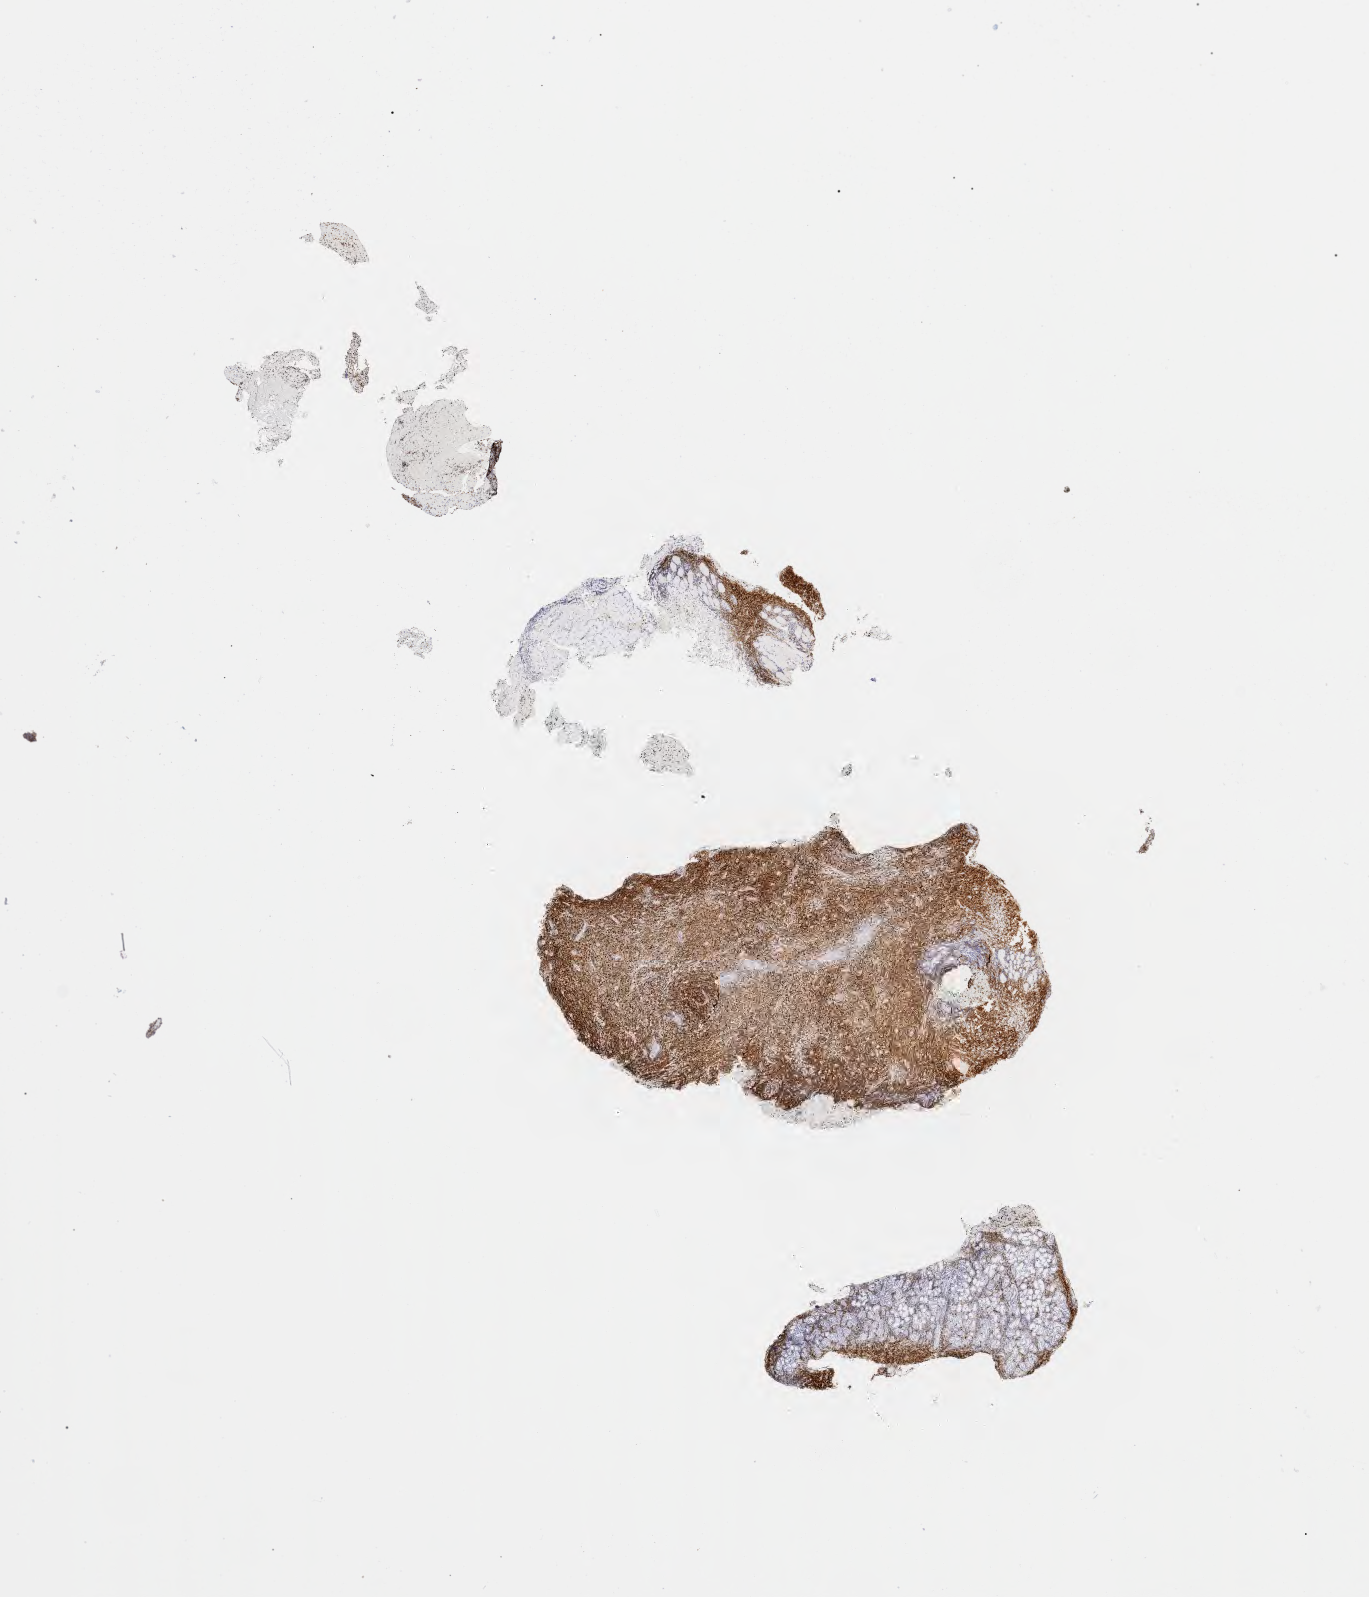
IHC for IRF4/MUM1, whole-slide image, shown as a low-resolution overview of the whole scanned area (about 11.1 x 12.9 mm). Specimen: tumor tissue. Male patient, aged 53.
Histologic diagnosis: Diffuse large B-cell lymphoma, NOS.